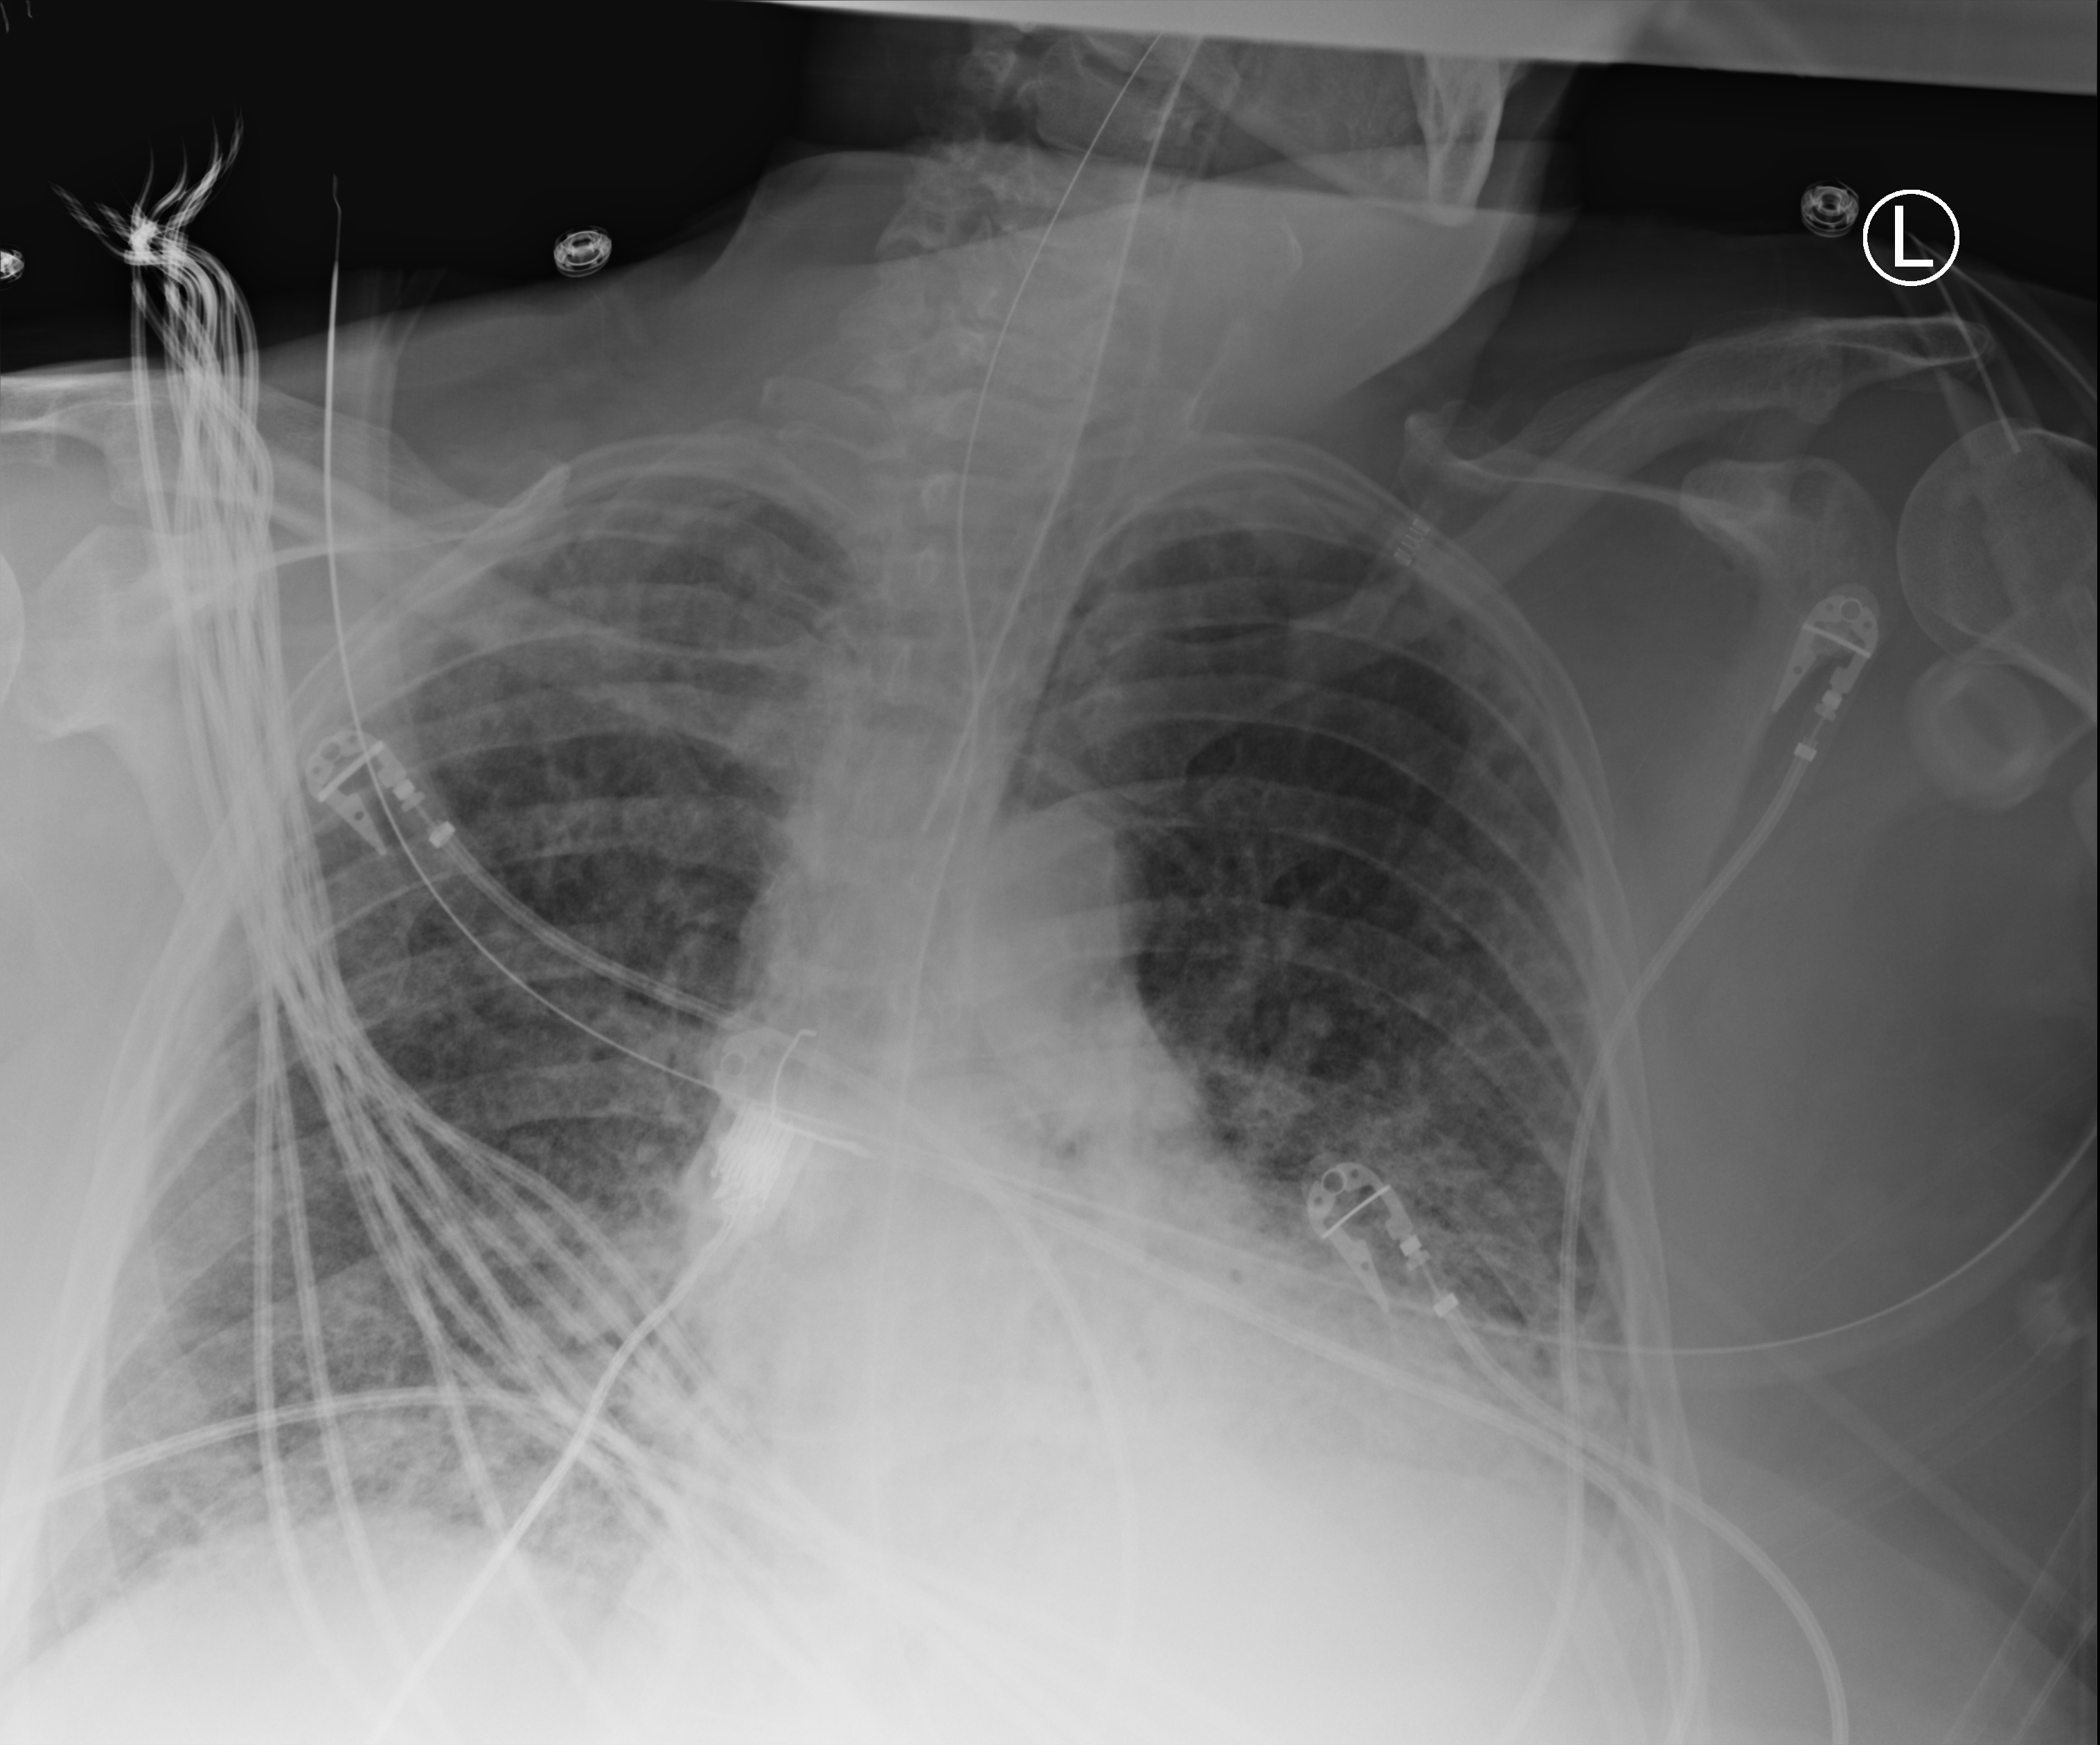
Chest X-ray (portable), anteroposterior (AP) projection. Patient hospitalised with COVID-19, aged 18–59 years.
From the hospital-stay record, not from the radiograph (when in the stay this image was taken is not recorded): length of hospital stay: 28 days; mechanically ventilated during this hospital stay: yes.